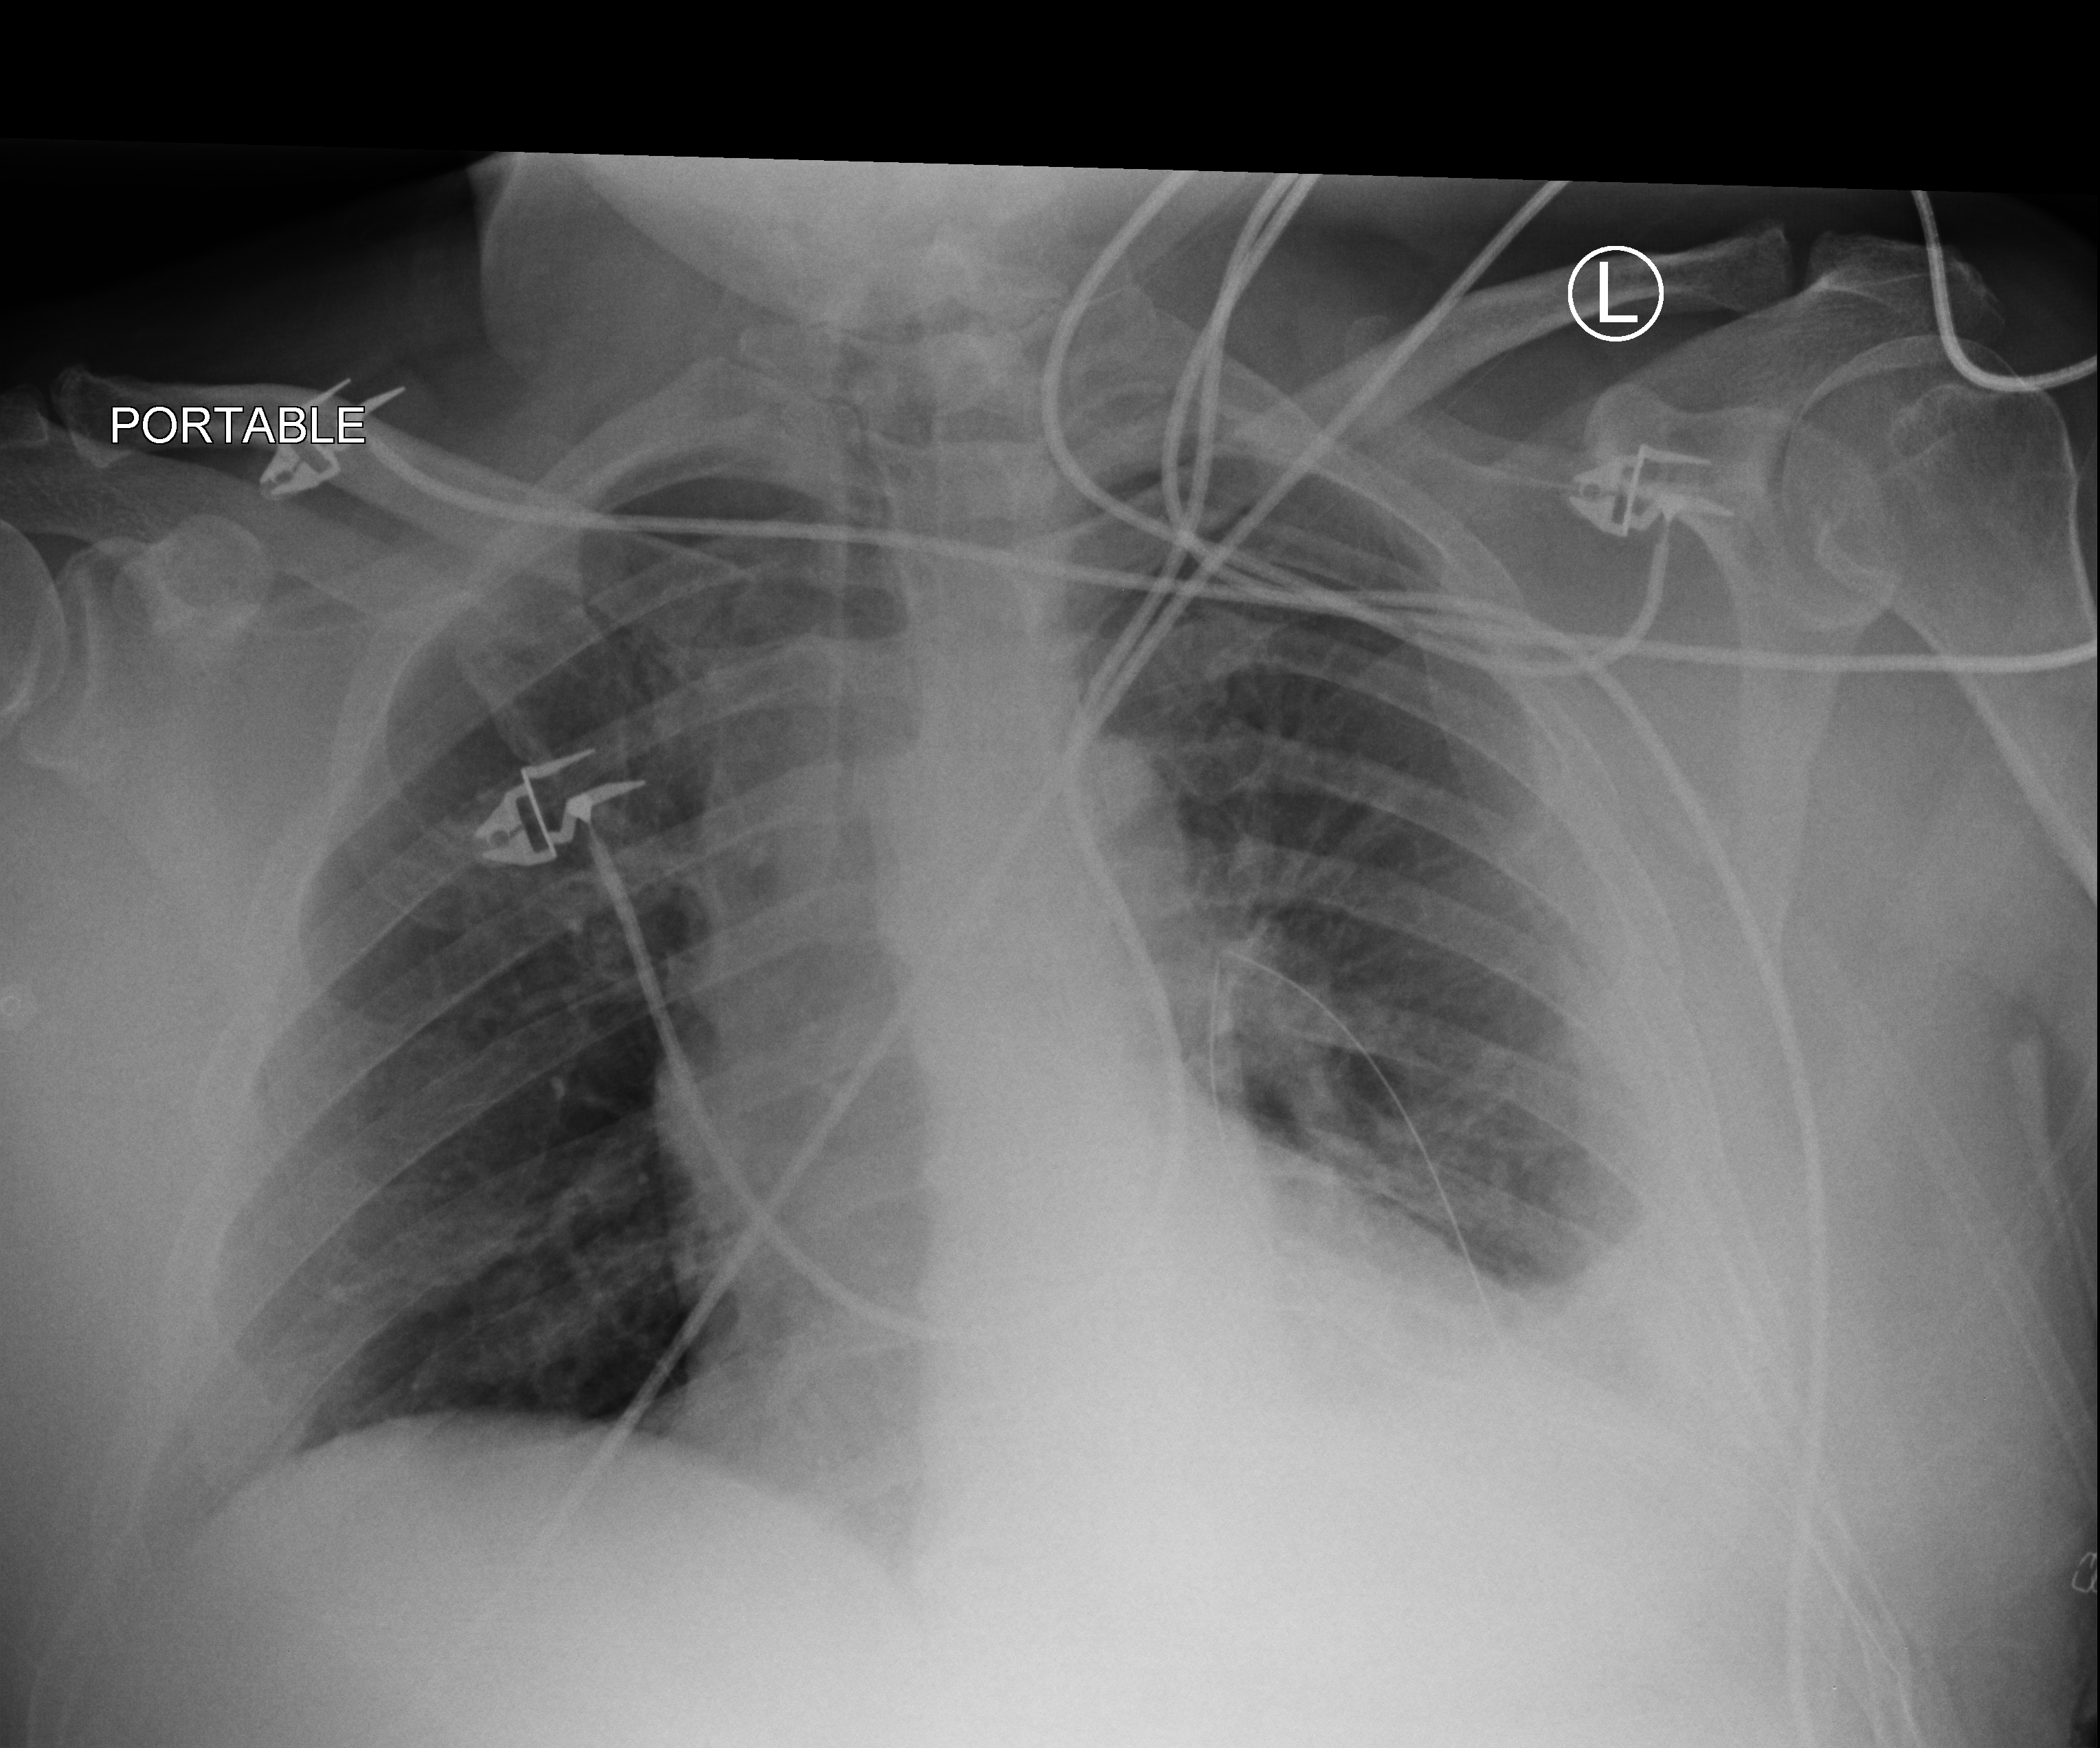
Portable chest radiograph. Male patient hospitalised with COVID-19, age 18–59 years.
From the hospital-stay record, not from the radiograph (when in the stay this image was taken is not recorded): mechanically ventilated during this hospital stay: no; admitted to intensive care during this hospital stay: no.